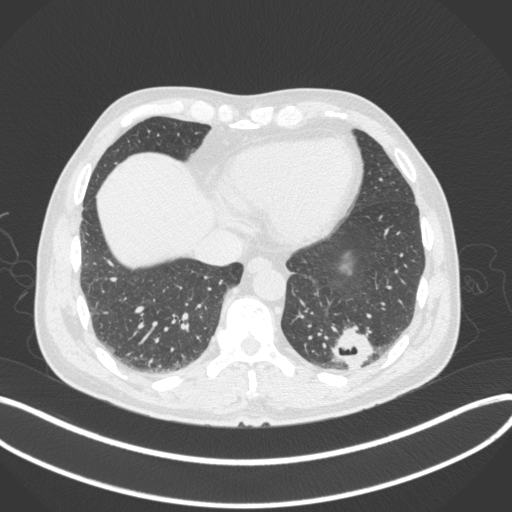
Chest CT, one axial slice; position 72 of 313 along the scan axis; 120 kVp; lung window (W 1500 / L -600 HU); 1 mm slice thickness; 512 × 512 image matrix, field of view 400 × 400 mm. Patient: male, 54 years. From the clinical record (not read from this slice): clinical TNM (as recorded): T1c N0 M1; histopathological grade: G3.
Outlined on this slice (rectangle marked by the reading radiologist):
- lung tumour (recorded histology: adenocarcinoma): bounding box <329,325,380,370> (left, top, right, bottom; pixels)